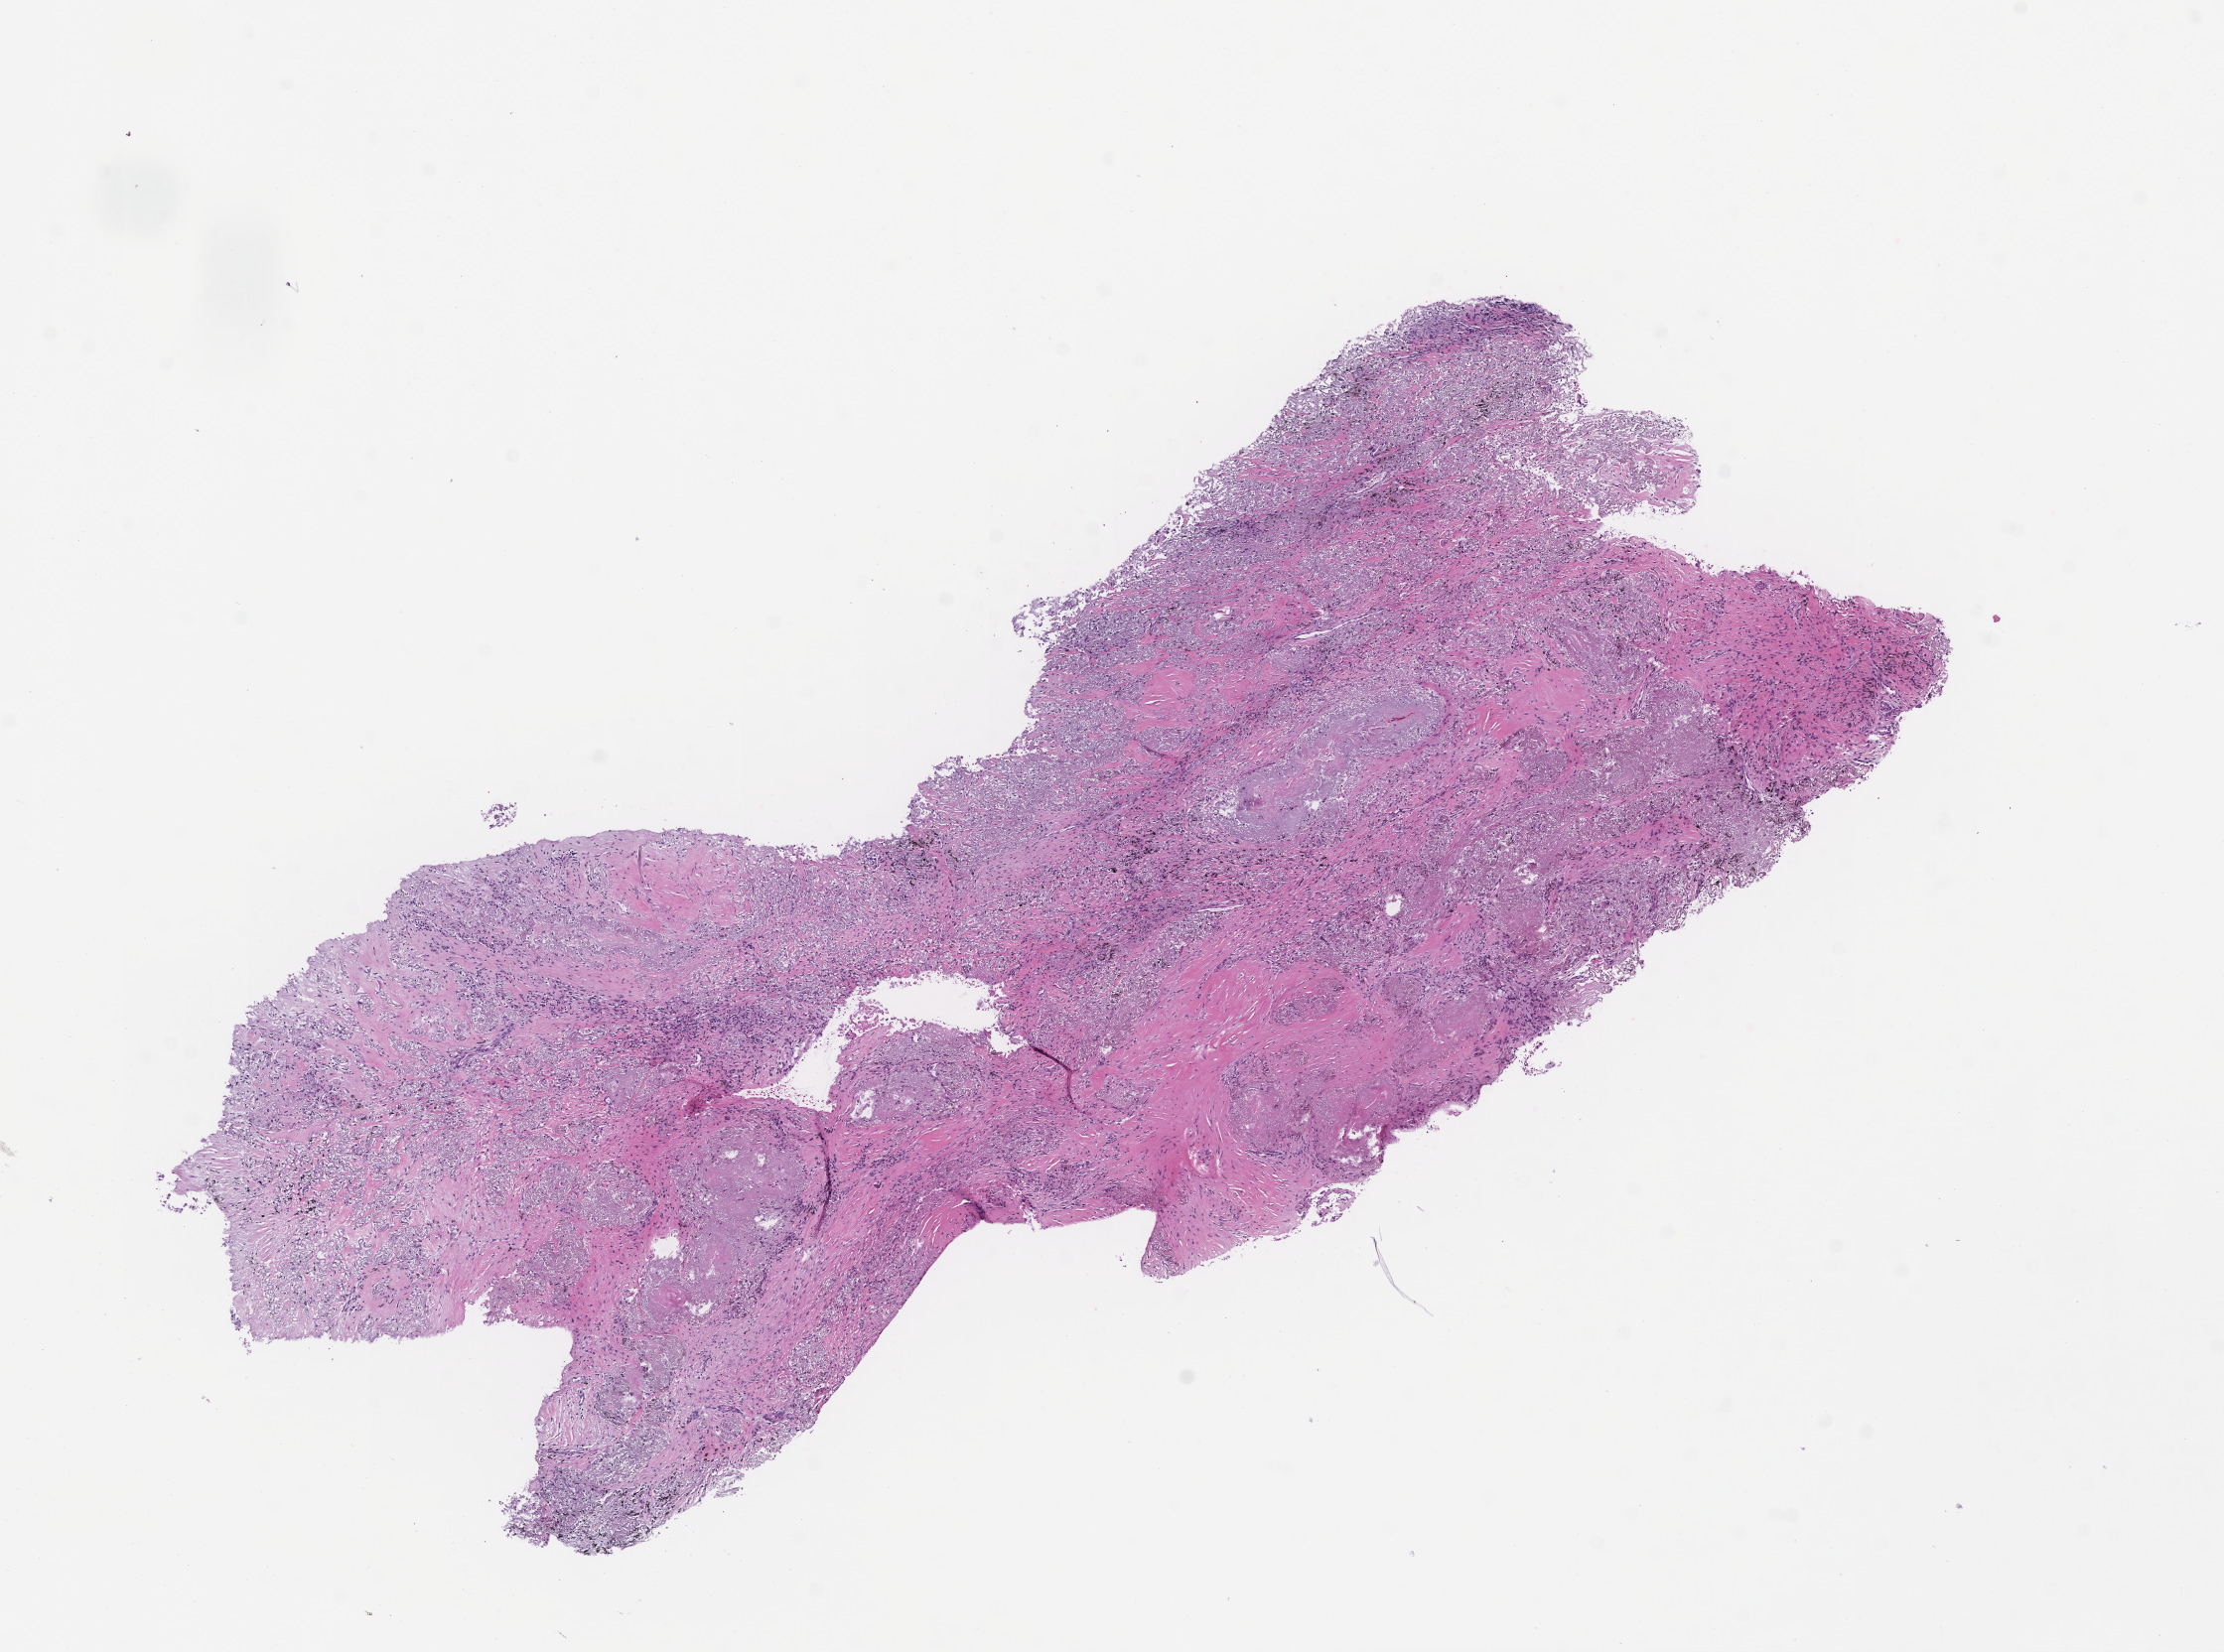
Whole-slide image, hematoxylin and eosin (H&E) stain, whole scanned area (about 9.0 x 6.7 mm) shown as a low-resolution overview, formalin-fixed, paraffin-embedded (FFPE) tissue, site: lung, collected at baseline (before treatment). Patient sex: male.
* this section: primary tumour tissue
* diagnosis: Non-Small Cell Lung Carcinoma